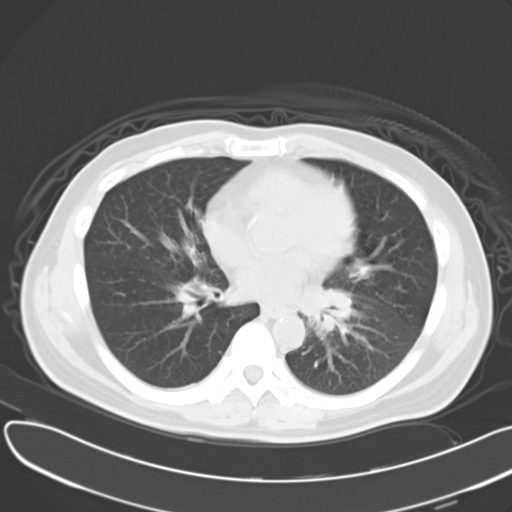
Chest CT, one axial slice. Slice 15 of 30 in the series (ordered by position). Reconstruction kernel B40f. Lung window (W 1500 / L -600 HU). 512 × 512 image matrix, field of view 376 × 376 mm. Male patient, age 55 years. From the clinical record (not read from this slice): clinical TNM (as recorded): T2 N3 M0; histopathological grade: G3.
Outlined on this slice (bounding box drawn by a radiologist):
- lung tumour (recorded histology: small cell carcinoma): bounding box (x1, y1, x2, y2) in pixels: (303, 281, 360, 333)